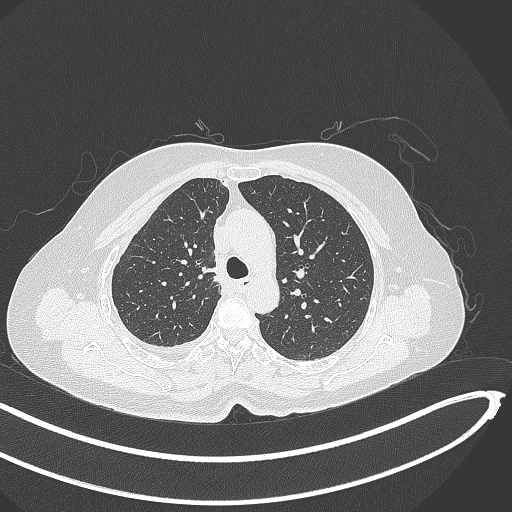
Chest CT, one axial slice. Slice 267 of 345 in the series (ordered by position). 120 kVp. Lung window (W 1500 / L -600 HU). 1 mm slice thickness. 512 × 512 image matrix. Female patient, age 64 years. Case-level facts recorded for this patient, not image findings: clinical TNM (as recorded): T1b N0 M1.
Outlined on this slice (bounding box drawn by a radiologist):
- lung tumour (recorded histology: adenocarcinoma): bounding box <197,262,219,283> (left, top, right, bottom; pixels)